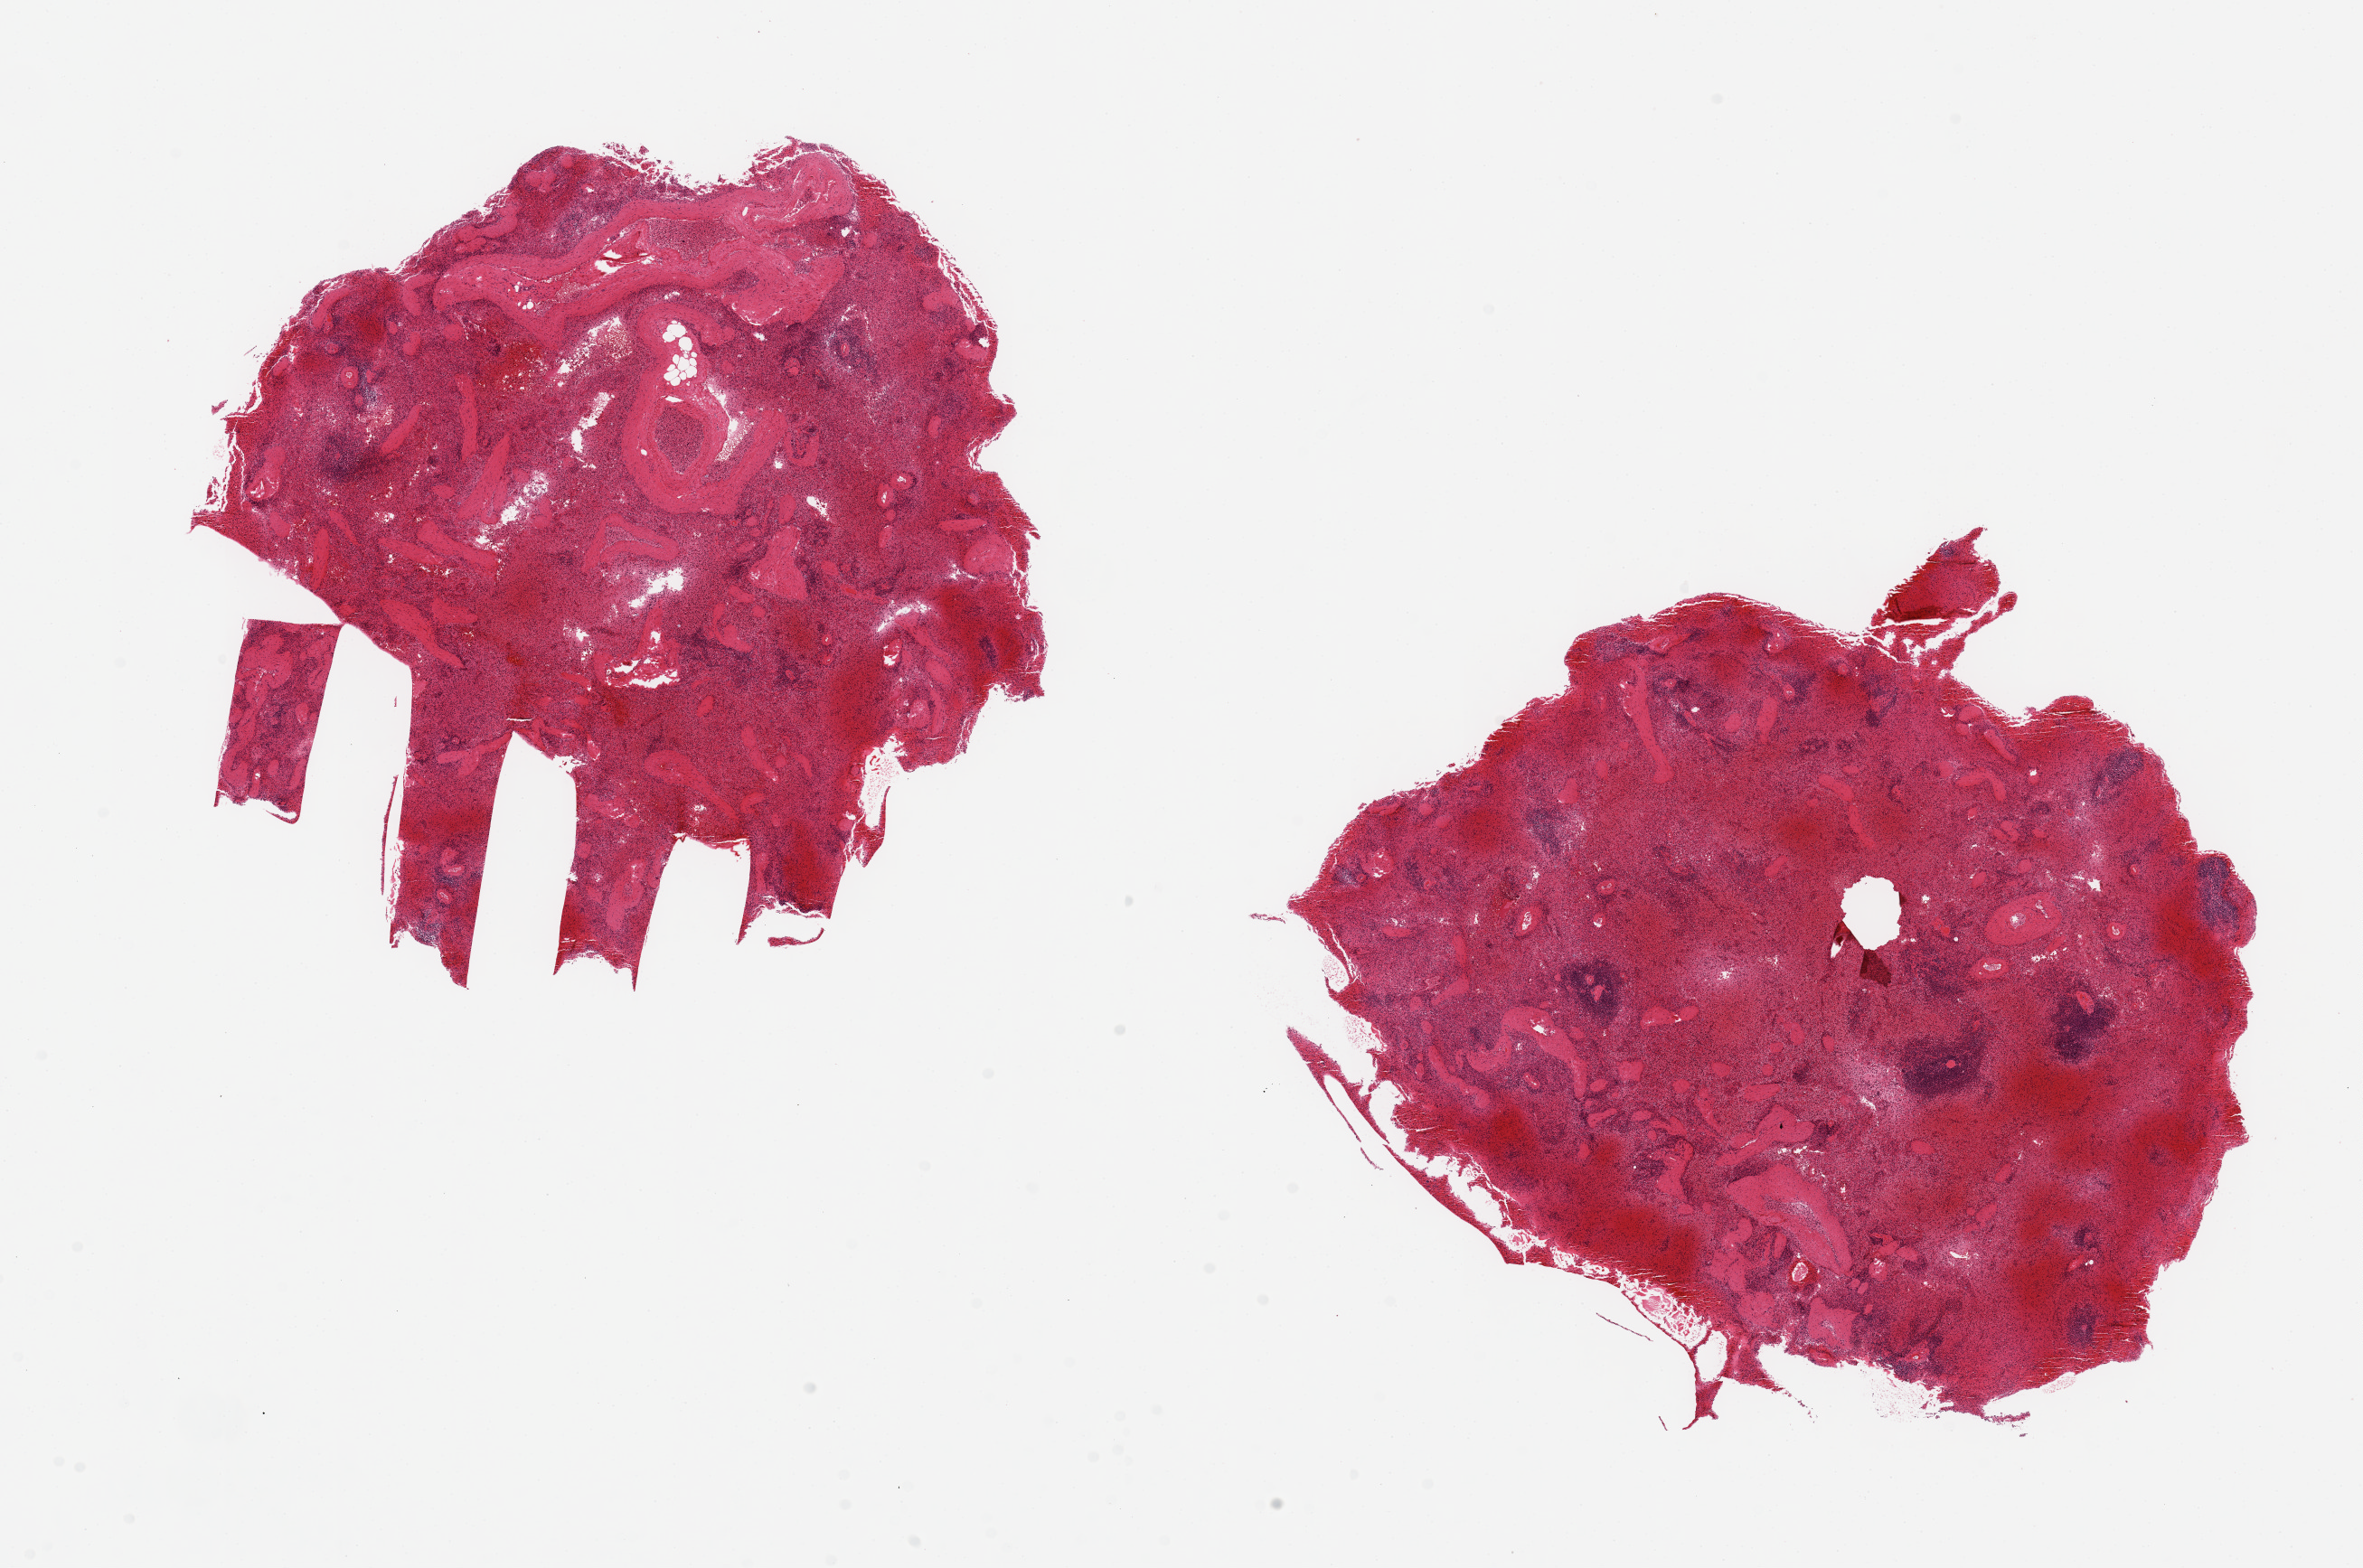
Hematoxylin and eosin (H&E) whole-slide image — a low-resolution overview of the entire scanned area, about 20.7 x 13.7 mm (acquisition: 20x scan), PAXgene-fixed, paraffin-embedded tissue, section of spleen (target tissue), tissue donor sample. Male donor.
Review note (as recorded): 2 aliquots, ~7x6mm Badly autolyzed/congested.